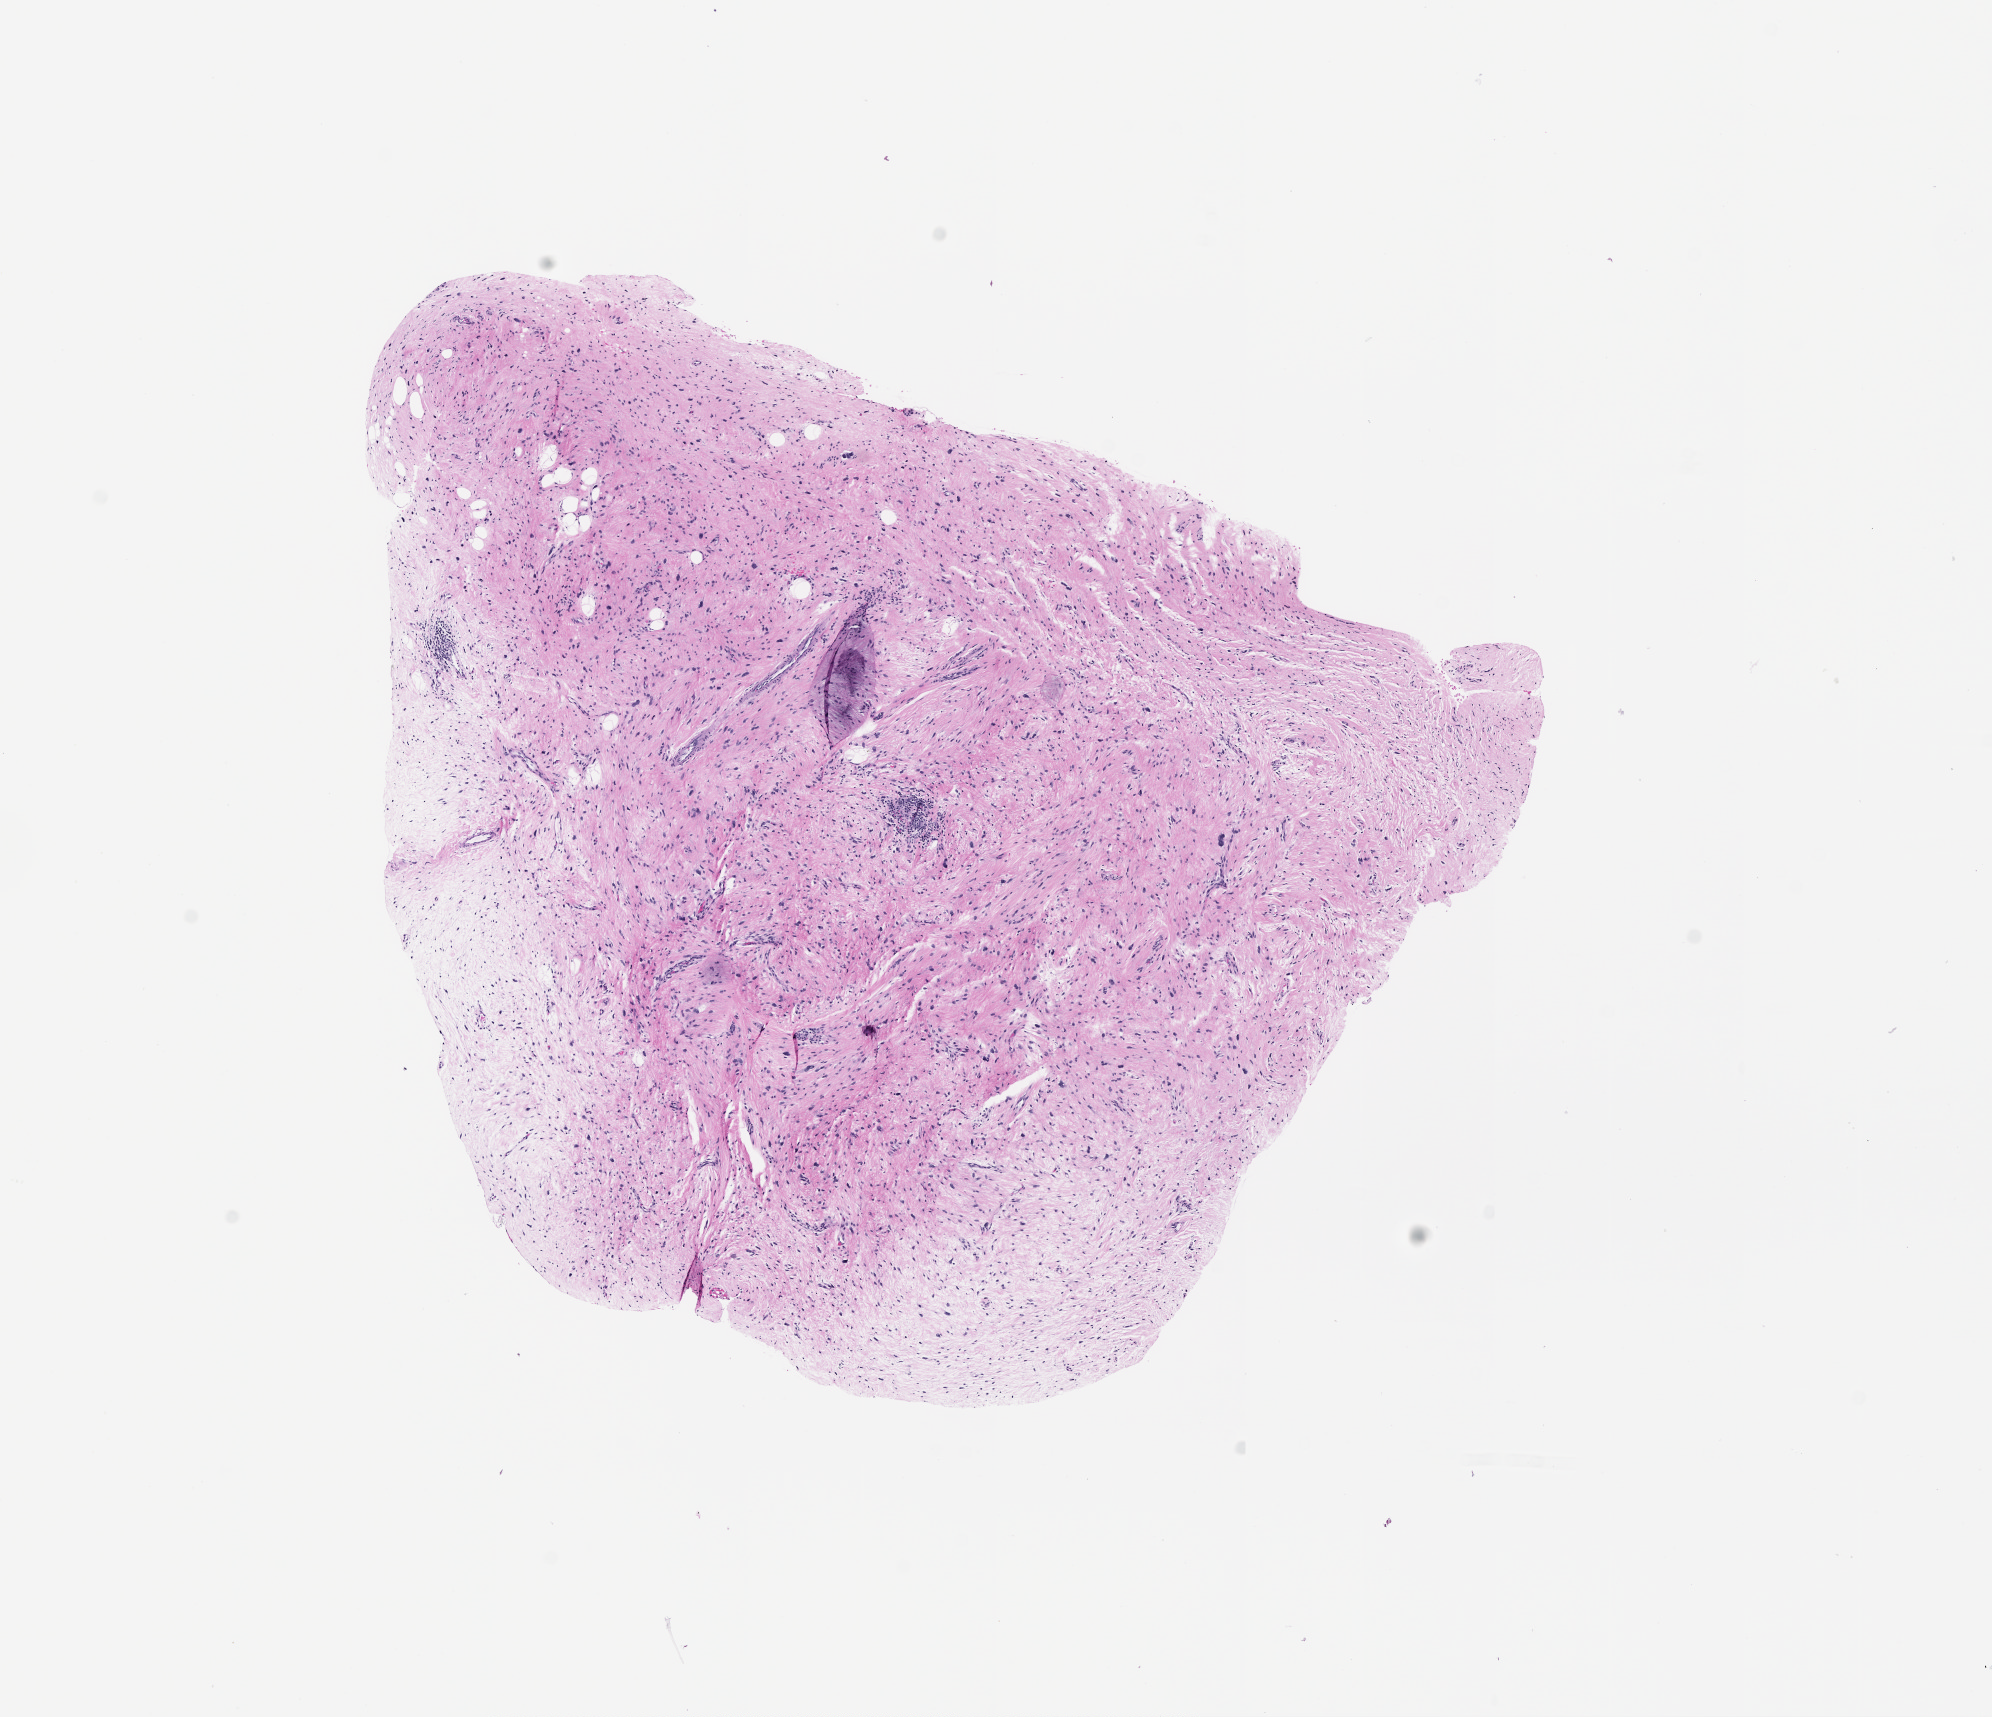
Digitized H&E tissue section (whole slide) — shown as a low-resolution overview of the whole scanned area (about 8.0 x 6.9 mm, from a 20x scan).
Patient diagnosis (cohort enrolment): sarcoma (site not recorded at cohort level).